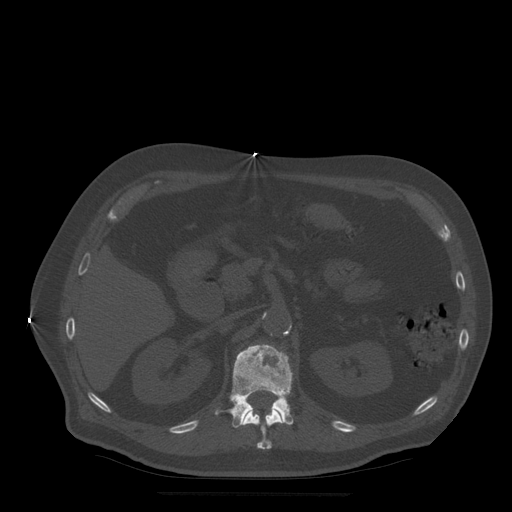
CT including the spine, one axial slice; slice 204 of 522 in the series (ordered by position); bone window (W 1800 / L 400 HU); 1.25 mm slice thickness; 512 × 512 image matrix, field of view 420 × 420 mm. Patient age 72 years. Case-level facts recorded for this patient, not image findings: primary cancer: prostate.
Outlined on this slice (semi-automatic segmentation, software-assisted and operator-edited):
- L1 vertebra: bounding box (x1, y1, x2, y2) in pixels: (216, 344, 294, 428)
- T12 vertebra: (244, 408, 283, 450)